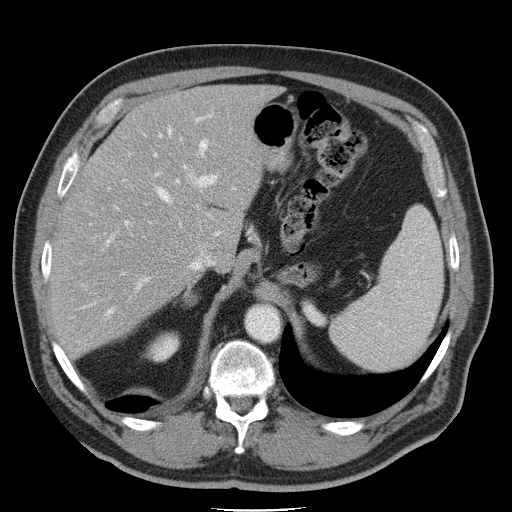
Contrast-enhanced abdominal CT, one axial slice; slice 32 of 45 in the series (ordered by position); 120 kVp; intravenous contrast given; soft-tissue window (W 400 / L 40 HU); 5 mm slice thickness; 512 × 512 image matrix, field of view 386 × 386 mm. Male patient, age 65 years. From the clinical record (not read from this slice): diagnosis: colorectal cancer liver metastases, imaged before liver resection; multiple liver metastases: yes; largest metastasis: 4.9 cm; disease in both lobes: no.
Structures marked on this image (manually delineated by an expert):
- hepatic veins: box from (x=82, y=126) to (x=214, y=337) px
- liver: (x=53, y=85)–(x=275, y=353)
- planned liver remnant (the part of the liver to remain after resection): (x=103, y=85)–(x=275, y=257)
- portal vein (with intrahepatic branches): (x=89, y=117)–(x=216, y=293)